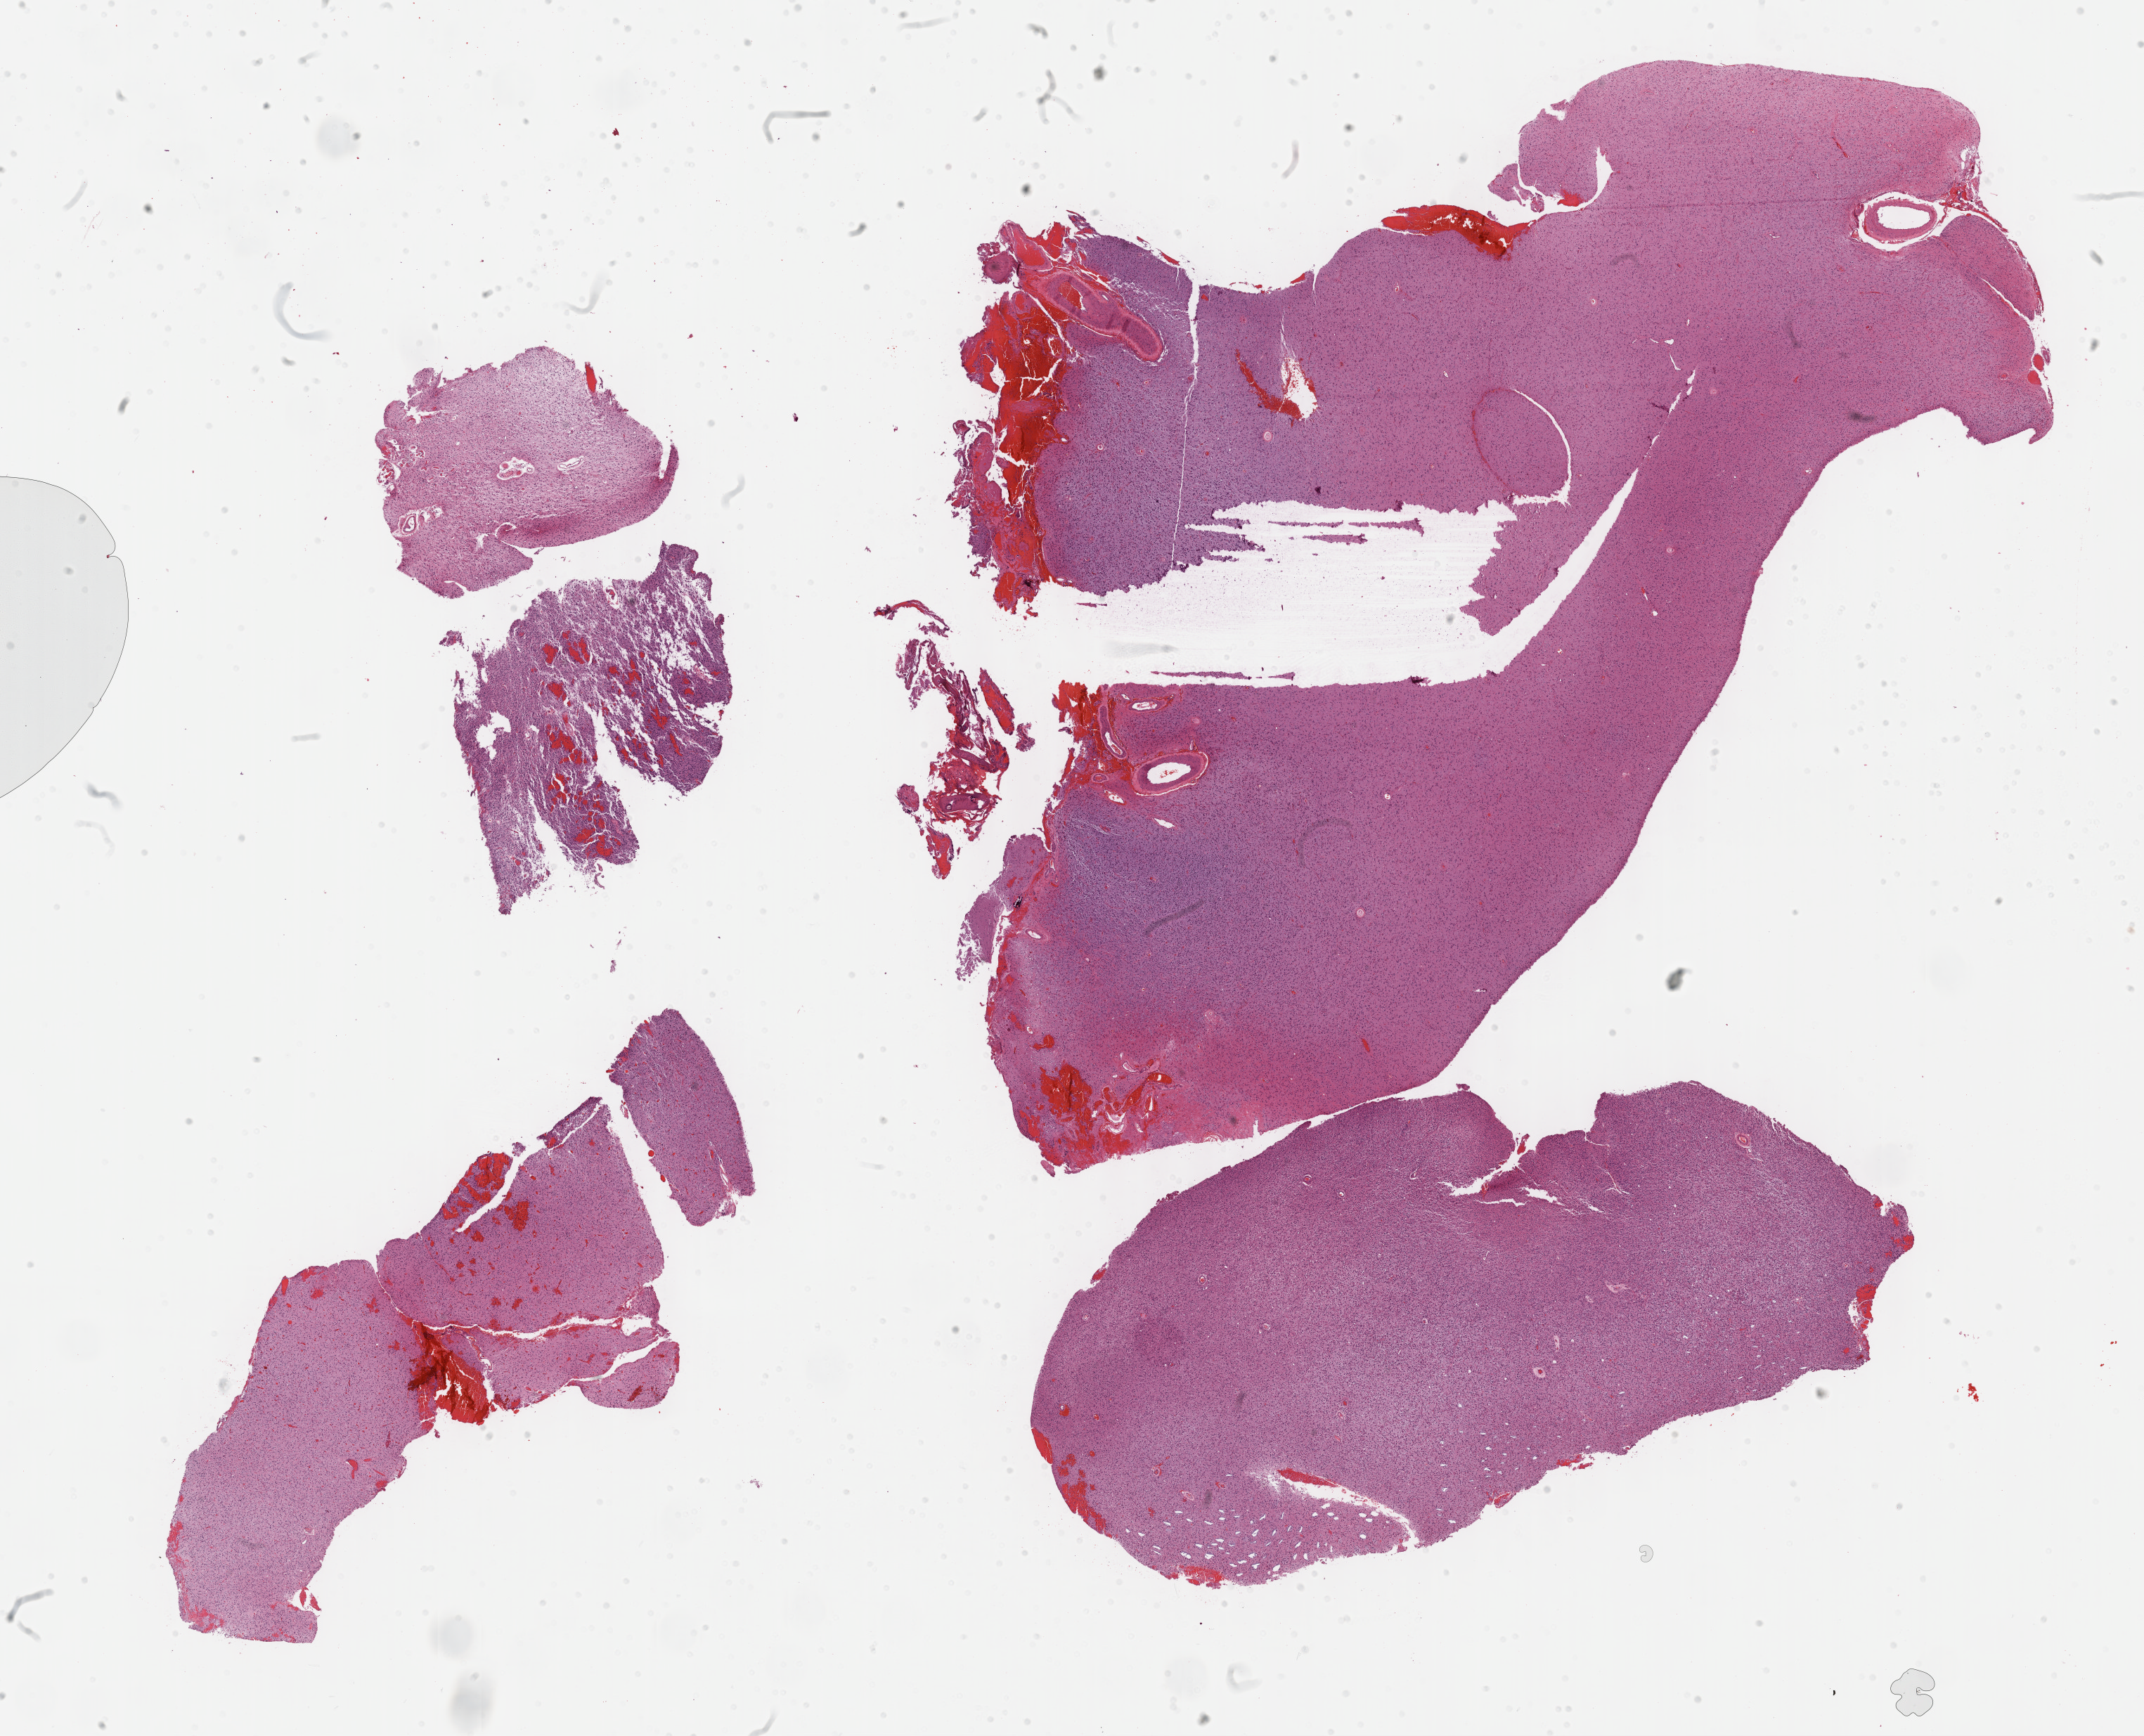
Digitized H&E-stained tissue section (whole slide) — whole scanned area (about 24.7 x 20.0 mm) shown as a low-resolution overview. Formalin-fixed paraffin-embedded (FFPE) diagnostic section. Brain, primary tumour sample. Female, age 58 years at initial diagnosis. Histologic grade: G2 (moderately differentiated).
Pathologic diagnosis: Oligodendroglioma, NOS (cerebrum).